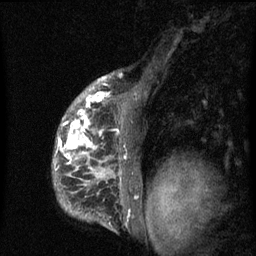
Breast MRI (dynamic contrast-enhanced), one sagittal slice. Position 48 of 60 along the scan axis. Dynamic contrast-enhanced series, image 2 of 3 at this slice position (ordered by acquisition). 1.5 T. TE 4.2 ms, TR 8 ms. 2 mm slice thickness. 256 × 256 image matrix. Patient: female, 50 years.
Outlined on this slice (semi-automatically segmented with operator editing):
- analysis volume of interest (the breast-tissue region the enhancement analysis was run in; not a lesion): bounding box (x1, y1, x2, y2) in pixels: (52, 90, 142, 216)
- tumour enhancement mask (voxels above the 70 % enhancement threshold inside the analysis volume of interest): (54, 91, 121, 186)